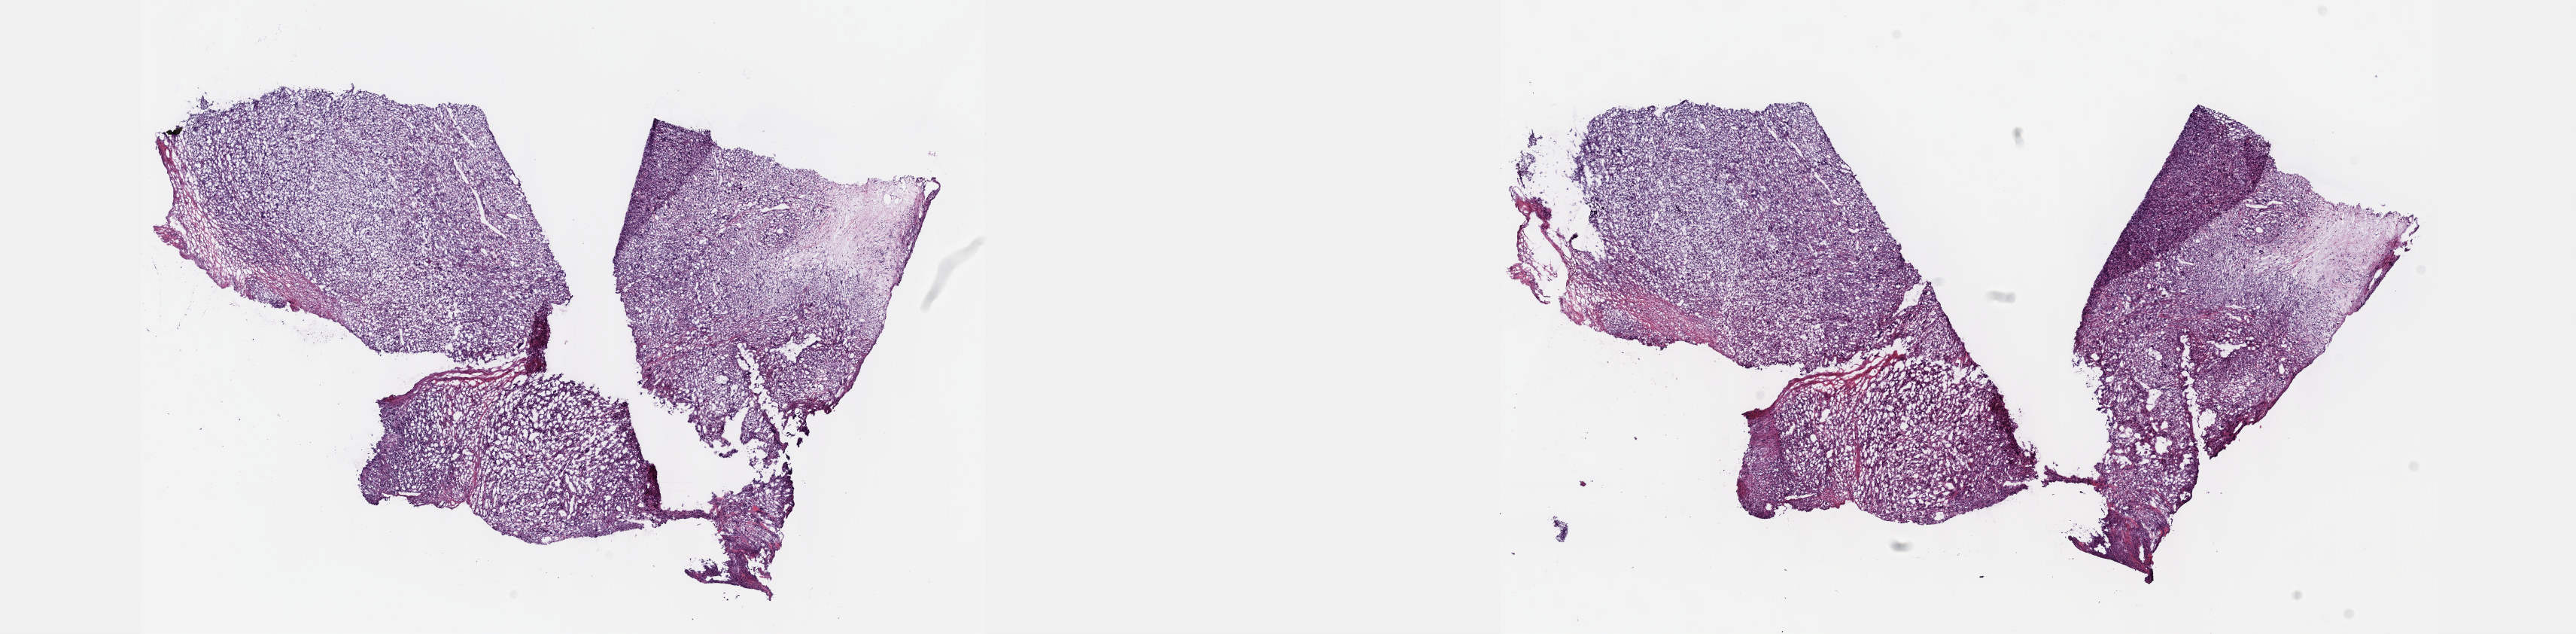
Hematoxylin and eosin (H&E) stained whole-slide image, shown as a low-resolution overview of the whole scanned area (about 27.7 x 6.8 mm); frozen section; retroperitoneum and peritoneum, primary tumour sample. Female, age 31 years at initial diagnosis. Composition of this section per pathologist review: tumour cells 85%, tumour nuclei 90%, normal cells 0%, stromal cells 15%, necrosis 0%. Infiltration values recorded for this section: lymphocyte infiltration 0%, monocyte infiltration 0%, neutrophil infiltration 0%.
* histologic diagnosis: Malignant peripheral nerve sheath tumor (retroperitoneum)